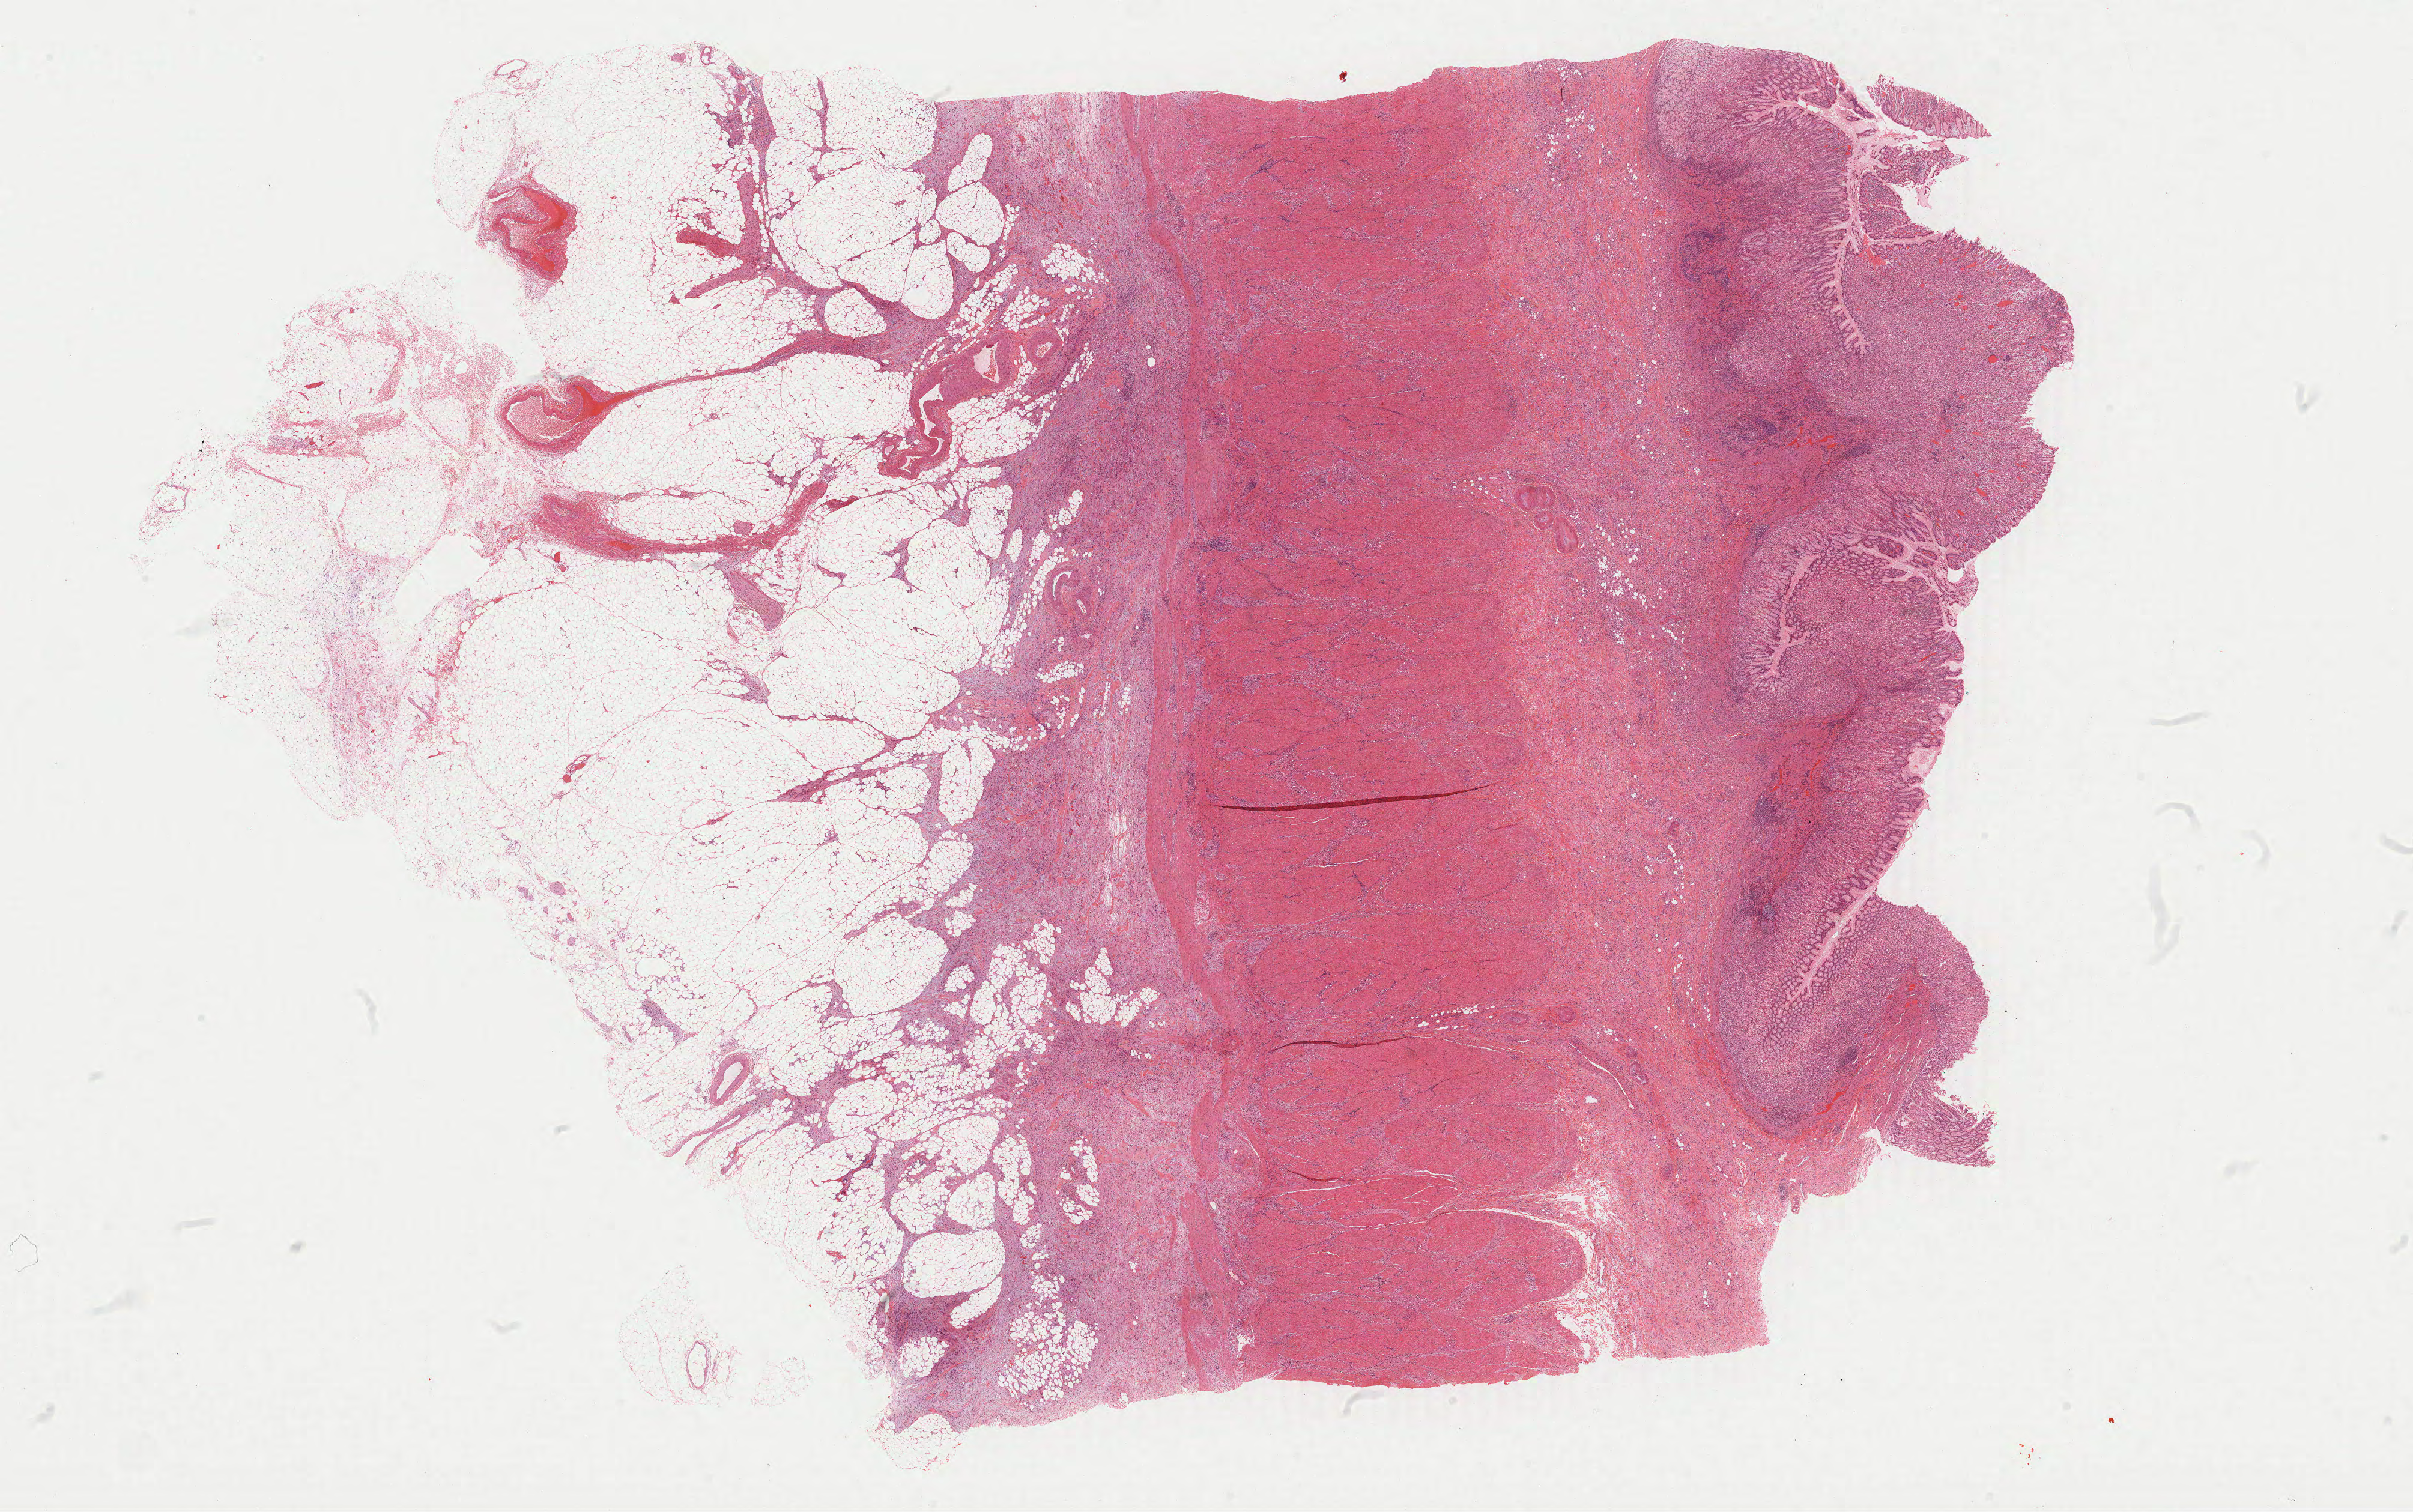
Whole-slide histology image, Hematoxylin and eosin (H&E) stained, low-resolution overview of the scanned area, about 32.3 x 20.2 mm, FFPE section, stomach, primary tumour sample. Female, age 68 years at initial diagnosis. Histologic grade: G3 (poorly differentiated).
Lymph nodes positive (case pathology): 0 of 23 examined. AJCC pathologic stage: IB (6th edition). Histologic diagnosis: Carcinoma, diffuse type (fundus of stomach).